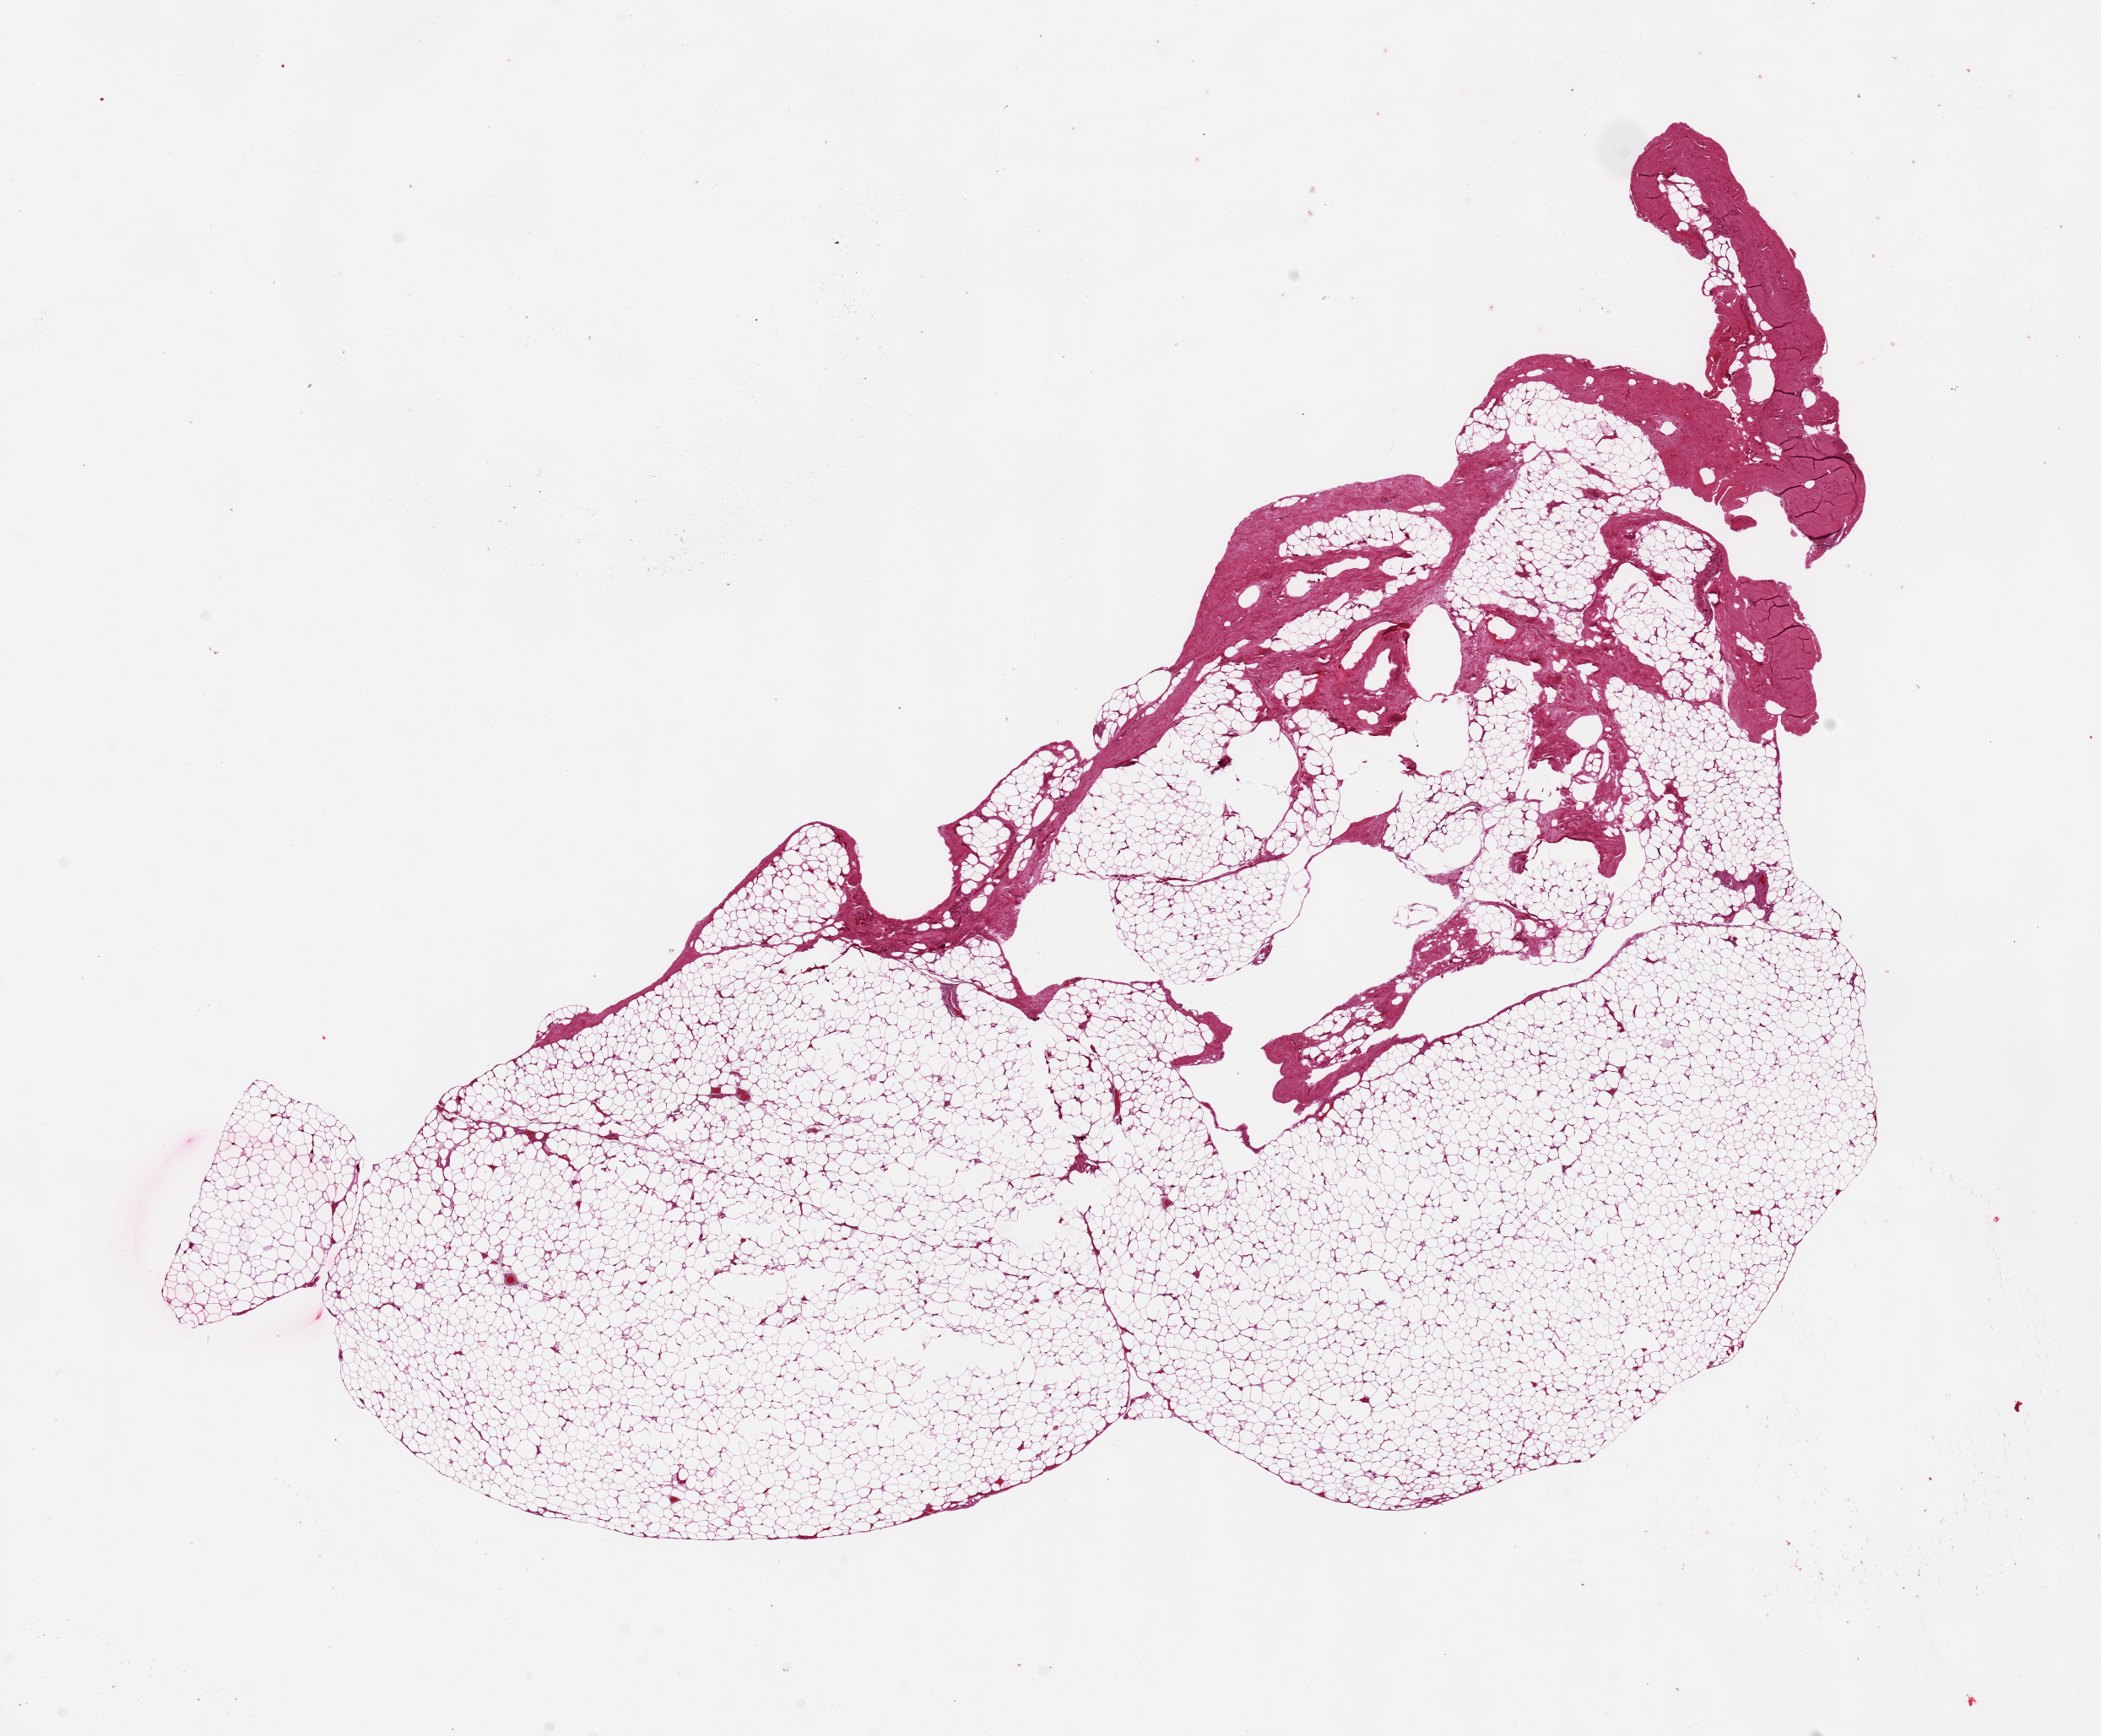
Whole-slide image, hematoxylin and eosin (H&E) stain, whole scanned area (about 19.7 x 16.3 mm) shown as a low-resolution overview; PAXgene-fixed, paraffin-embedded tissue; section of adipose tissue (target tissue); donor tissue sample. Donor: male.
* review note (as recorded): 90% adipose, 10% stroma